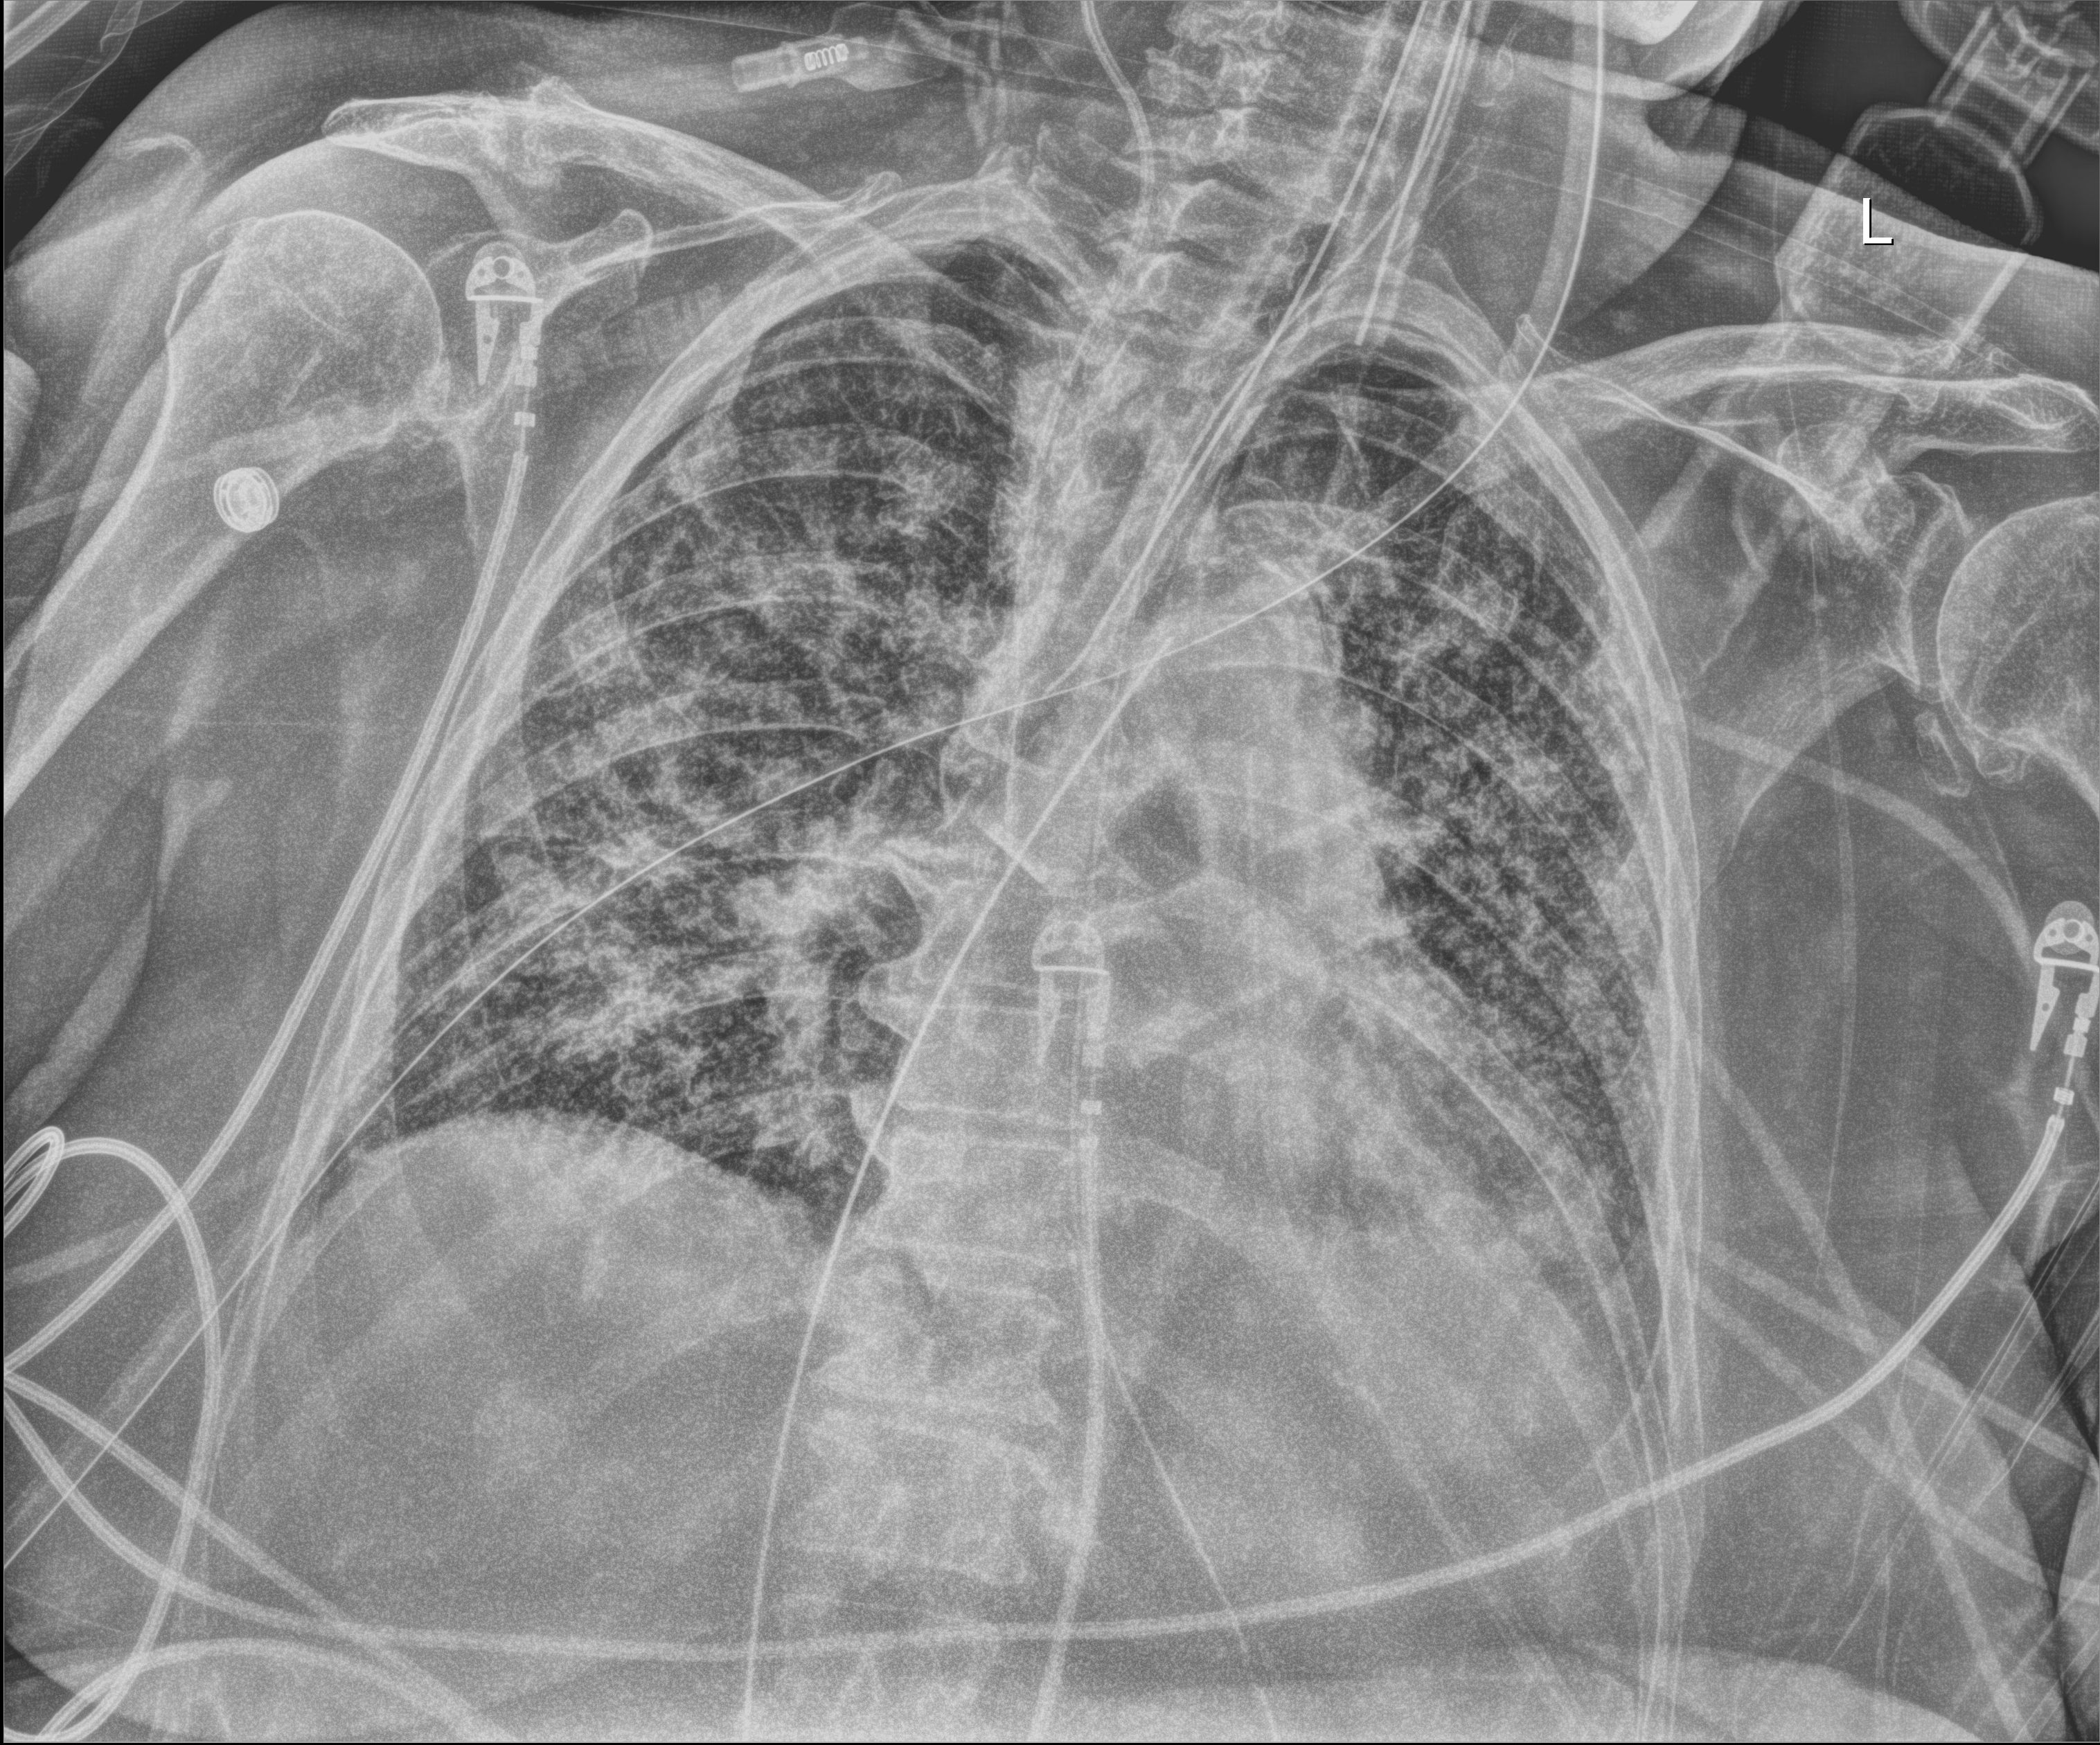
Bedside chest radiograph (digital radiography), anteroposterior (AP) projection. Patient hospitalised with COVID-19; female, aged 75–90 years.
From the hospital-stay record, not from the radiograph (when in the stay this image was taken is not recorded):
- mechanically ventilated during this hospital stay: yes
- length of hospital stay: 56 days